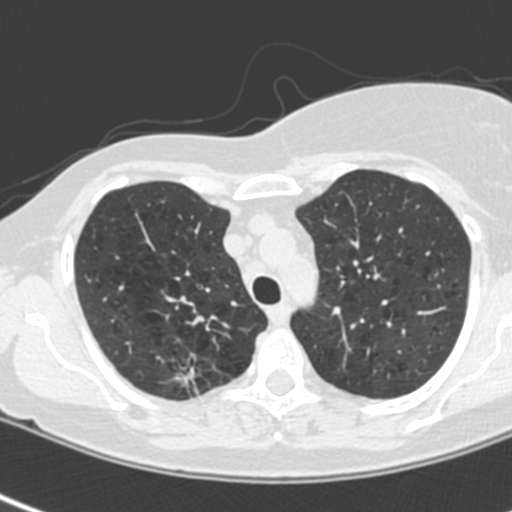
Low-dose screening chest CT, one axial slice. Position 172 of 214 along the scan axis. 120 kVp. Lung window (W 1500 / L -600 HU). 1.3 mm slice thickness. 512 × 512 image matrix, field of view 281 × 281 mm.
Outlined on this slice (expert manual segmentation):
- lesion 1 (tumor, upper lobe of right lung): bounding box (x1, y1, x2, y2) in pixels: (176, 368, 195, 386)